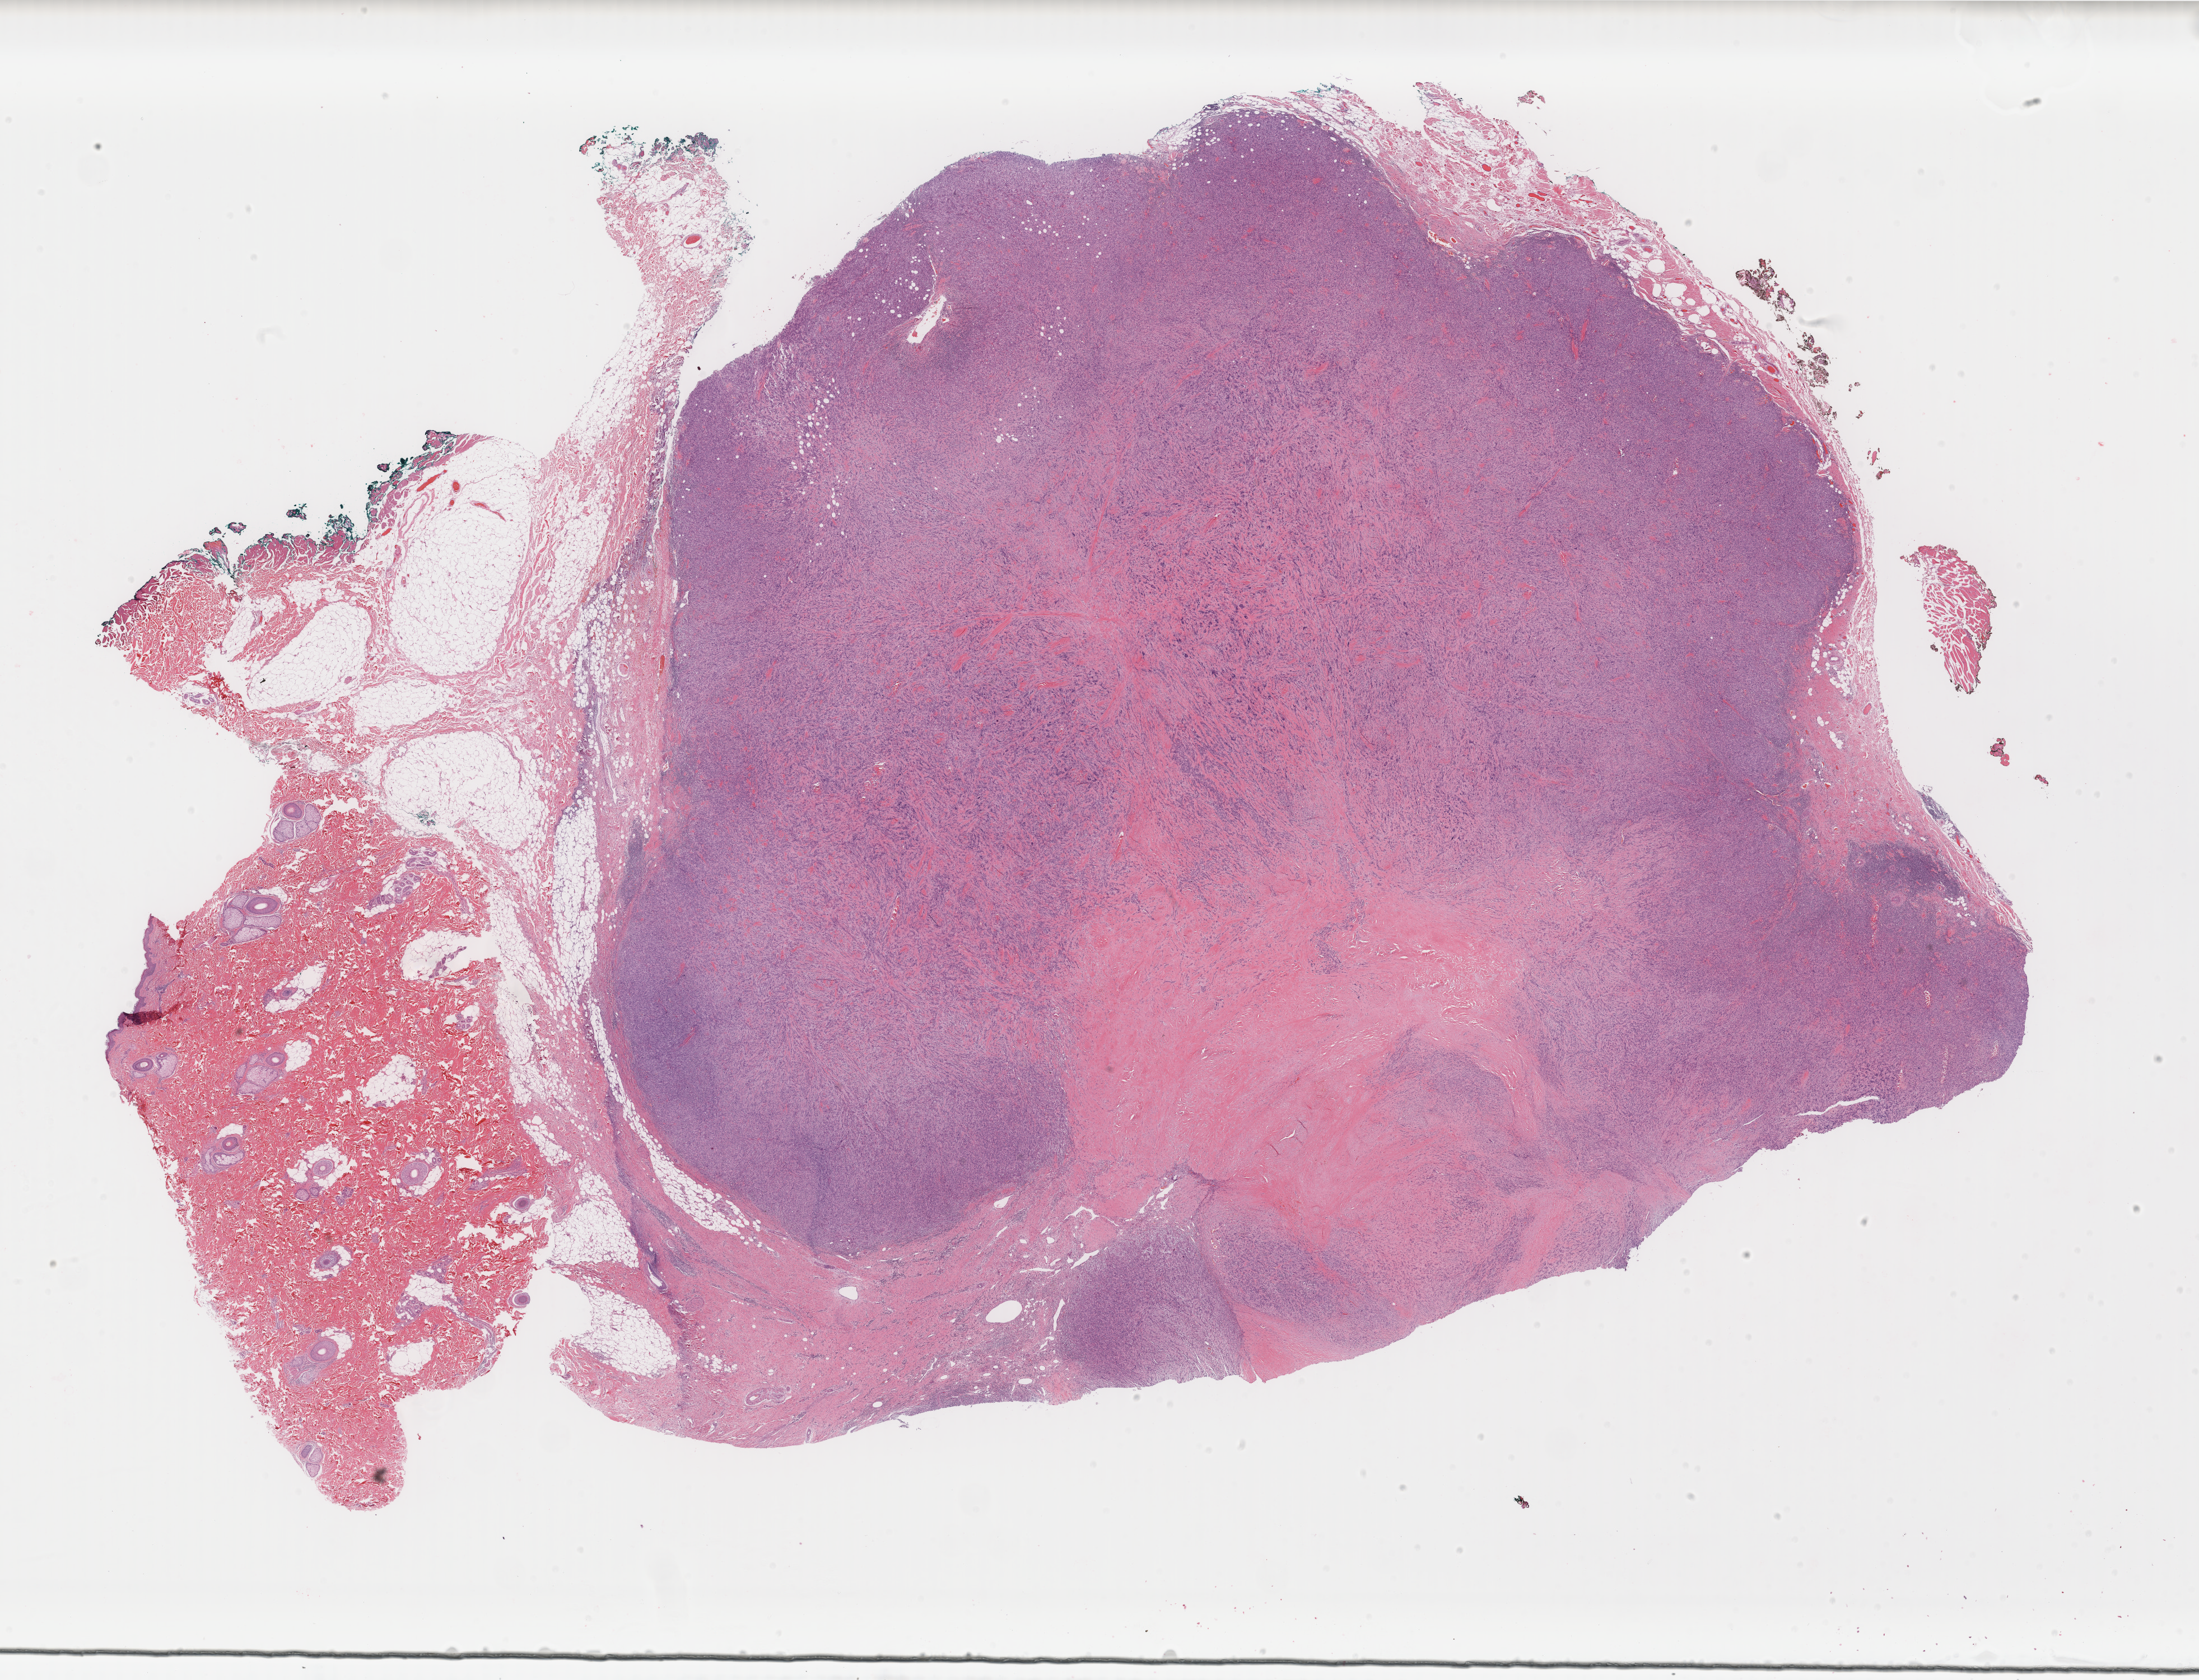
H&E-stained whole-slide image — shown as a low-resolution overview of the whole scanned area (about 31.2 x 23.8 mm); FFPE section; metastatic tumour sample. Male, age 45 years at initial diagnosis.
- this section: metastatic tumour tissue
- patient diagnosis: Malignant melanoma, NOS